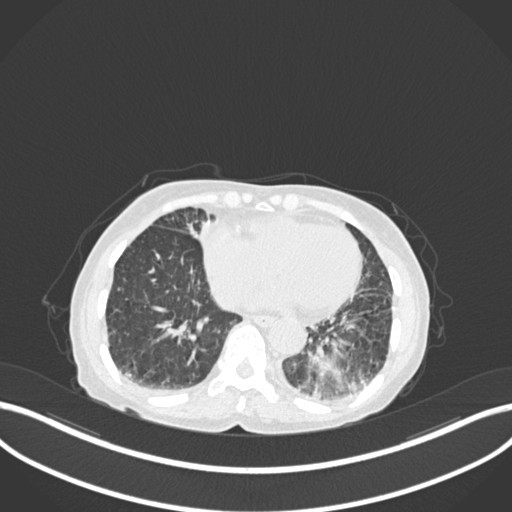
Chest CT, one axial slice. Position 35 of 233 along the scan axis. Reconstruction kernel B30f. Lung window (W 1500 / L -600 HU). 1 mm slice thickness. 512 × 512 image matrix, field of view 400 × 400 mm. Patient: female, 78 years. Case-level facts recorded for this patient, not image findings: clinical TNM (as recorded): T3 N0 M1.
Structures marked on this image (rectangle marked by the reading radiologist):
- lung tumour (recorded histology: squamous cell carcinoma): bounding box [x1, y1, x2, y2] px = [300, 336, 357, 401]